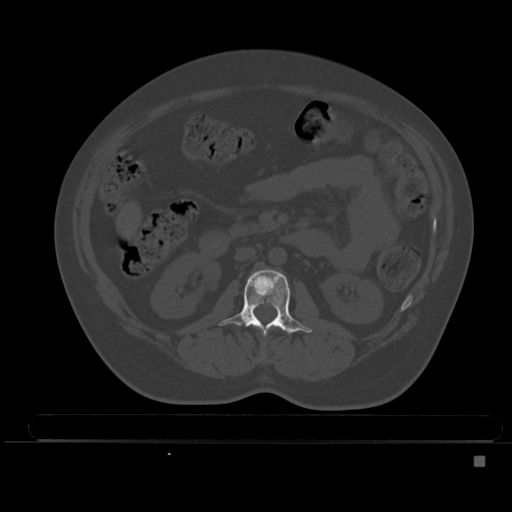
CT including the spine, one axial slice; slice 175 of 495 in the series (ordered by position); bone window (W 1800 / L 400 HU); 1.5 mm slice thickness; 512 × 512 image matrix, field of view 404 × 404 mm. Patient: female, 33 years. Case-level facts recorded for this patient, not image findings: primary cancer: breast.
Annotated regions visible in this slice (semi-automatic segmentation, software-assisted and operator-edited):
- L2 vertebra: bounding box <218,269,312,335> (left, top, right, bottom; pixels)